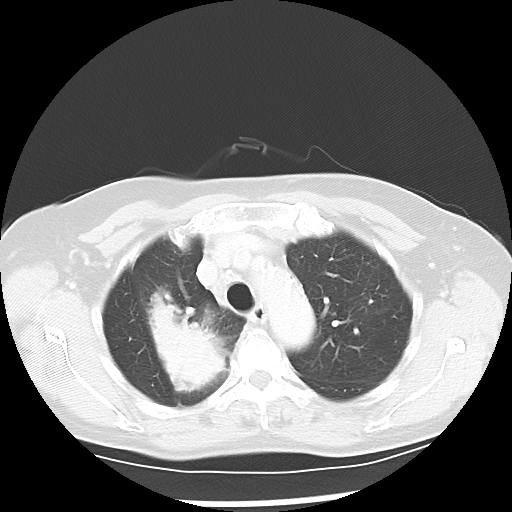
Chest CT, one axial slice; reconstruction kernel LUNG; 100 kVp; lung window (W 1500 / L -600 HU); 5 mm slice thickness; 512 × 512 image matrix, field of view 328 × 328 mm. Patient: female, 60 years. Case-level facts recorded for this patient, not image findings: clinical TNM (as recorded): T2 N1 M1a.
Structures marked on this image (bounding box drawn by a radiologist):
- lung tumour (recorded histology: adenocarcinoma): bounding box (x1, y1, x2, y2) in pixels: (139, 281, 228, 398)